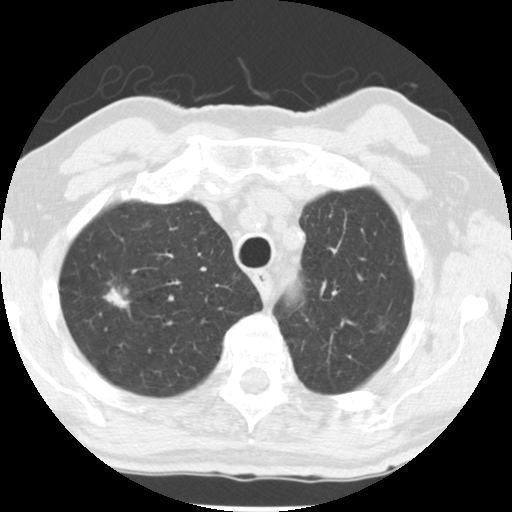
Low-dose screening chest CT, axial slice. Baseline screening round. Lung window (W 1500 / L -600 HU). 2.5 mm slice thickness. Standard (soft-tissue) reconstruction kernel (STANDARD). 512 × 512 image matrix, field of view 313 × 313 mm. Male, age 69 years at enrolment. Former smoker at enrolment.
Expert-annotated lung lesion, bounding box (x1, y1, x2, y2) in pixels: (90, 271, 148, 329). The screening reader recorded 2 non-calcified nodules or masses ≥4 mm on this exam (right upper lobe, left upper lobe); which of them this box marks is not recorded. Official screen result: positive, change unspecified: nodule(s) >= 4 mm or enlarging nodule(s), mass(es), or other non-specific abnormalities suspicious for lung cancer. Later outcome: lung cancer diagnosed 105 days after this screen — adenocarcinoma, NOS, right upper lobe, well differentiated (G1), stage IA (AJCC 6th edition), 17 mm at pathology.